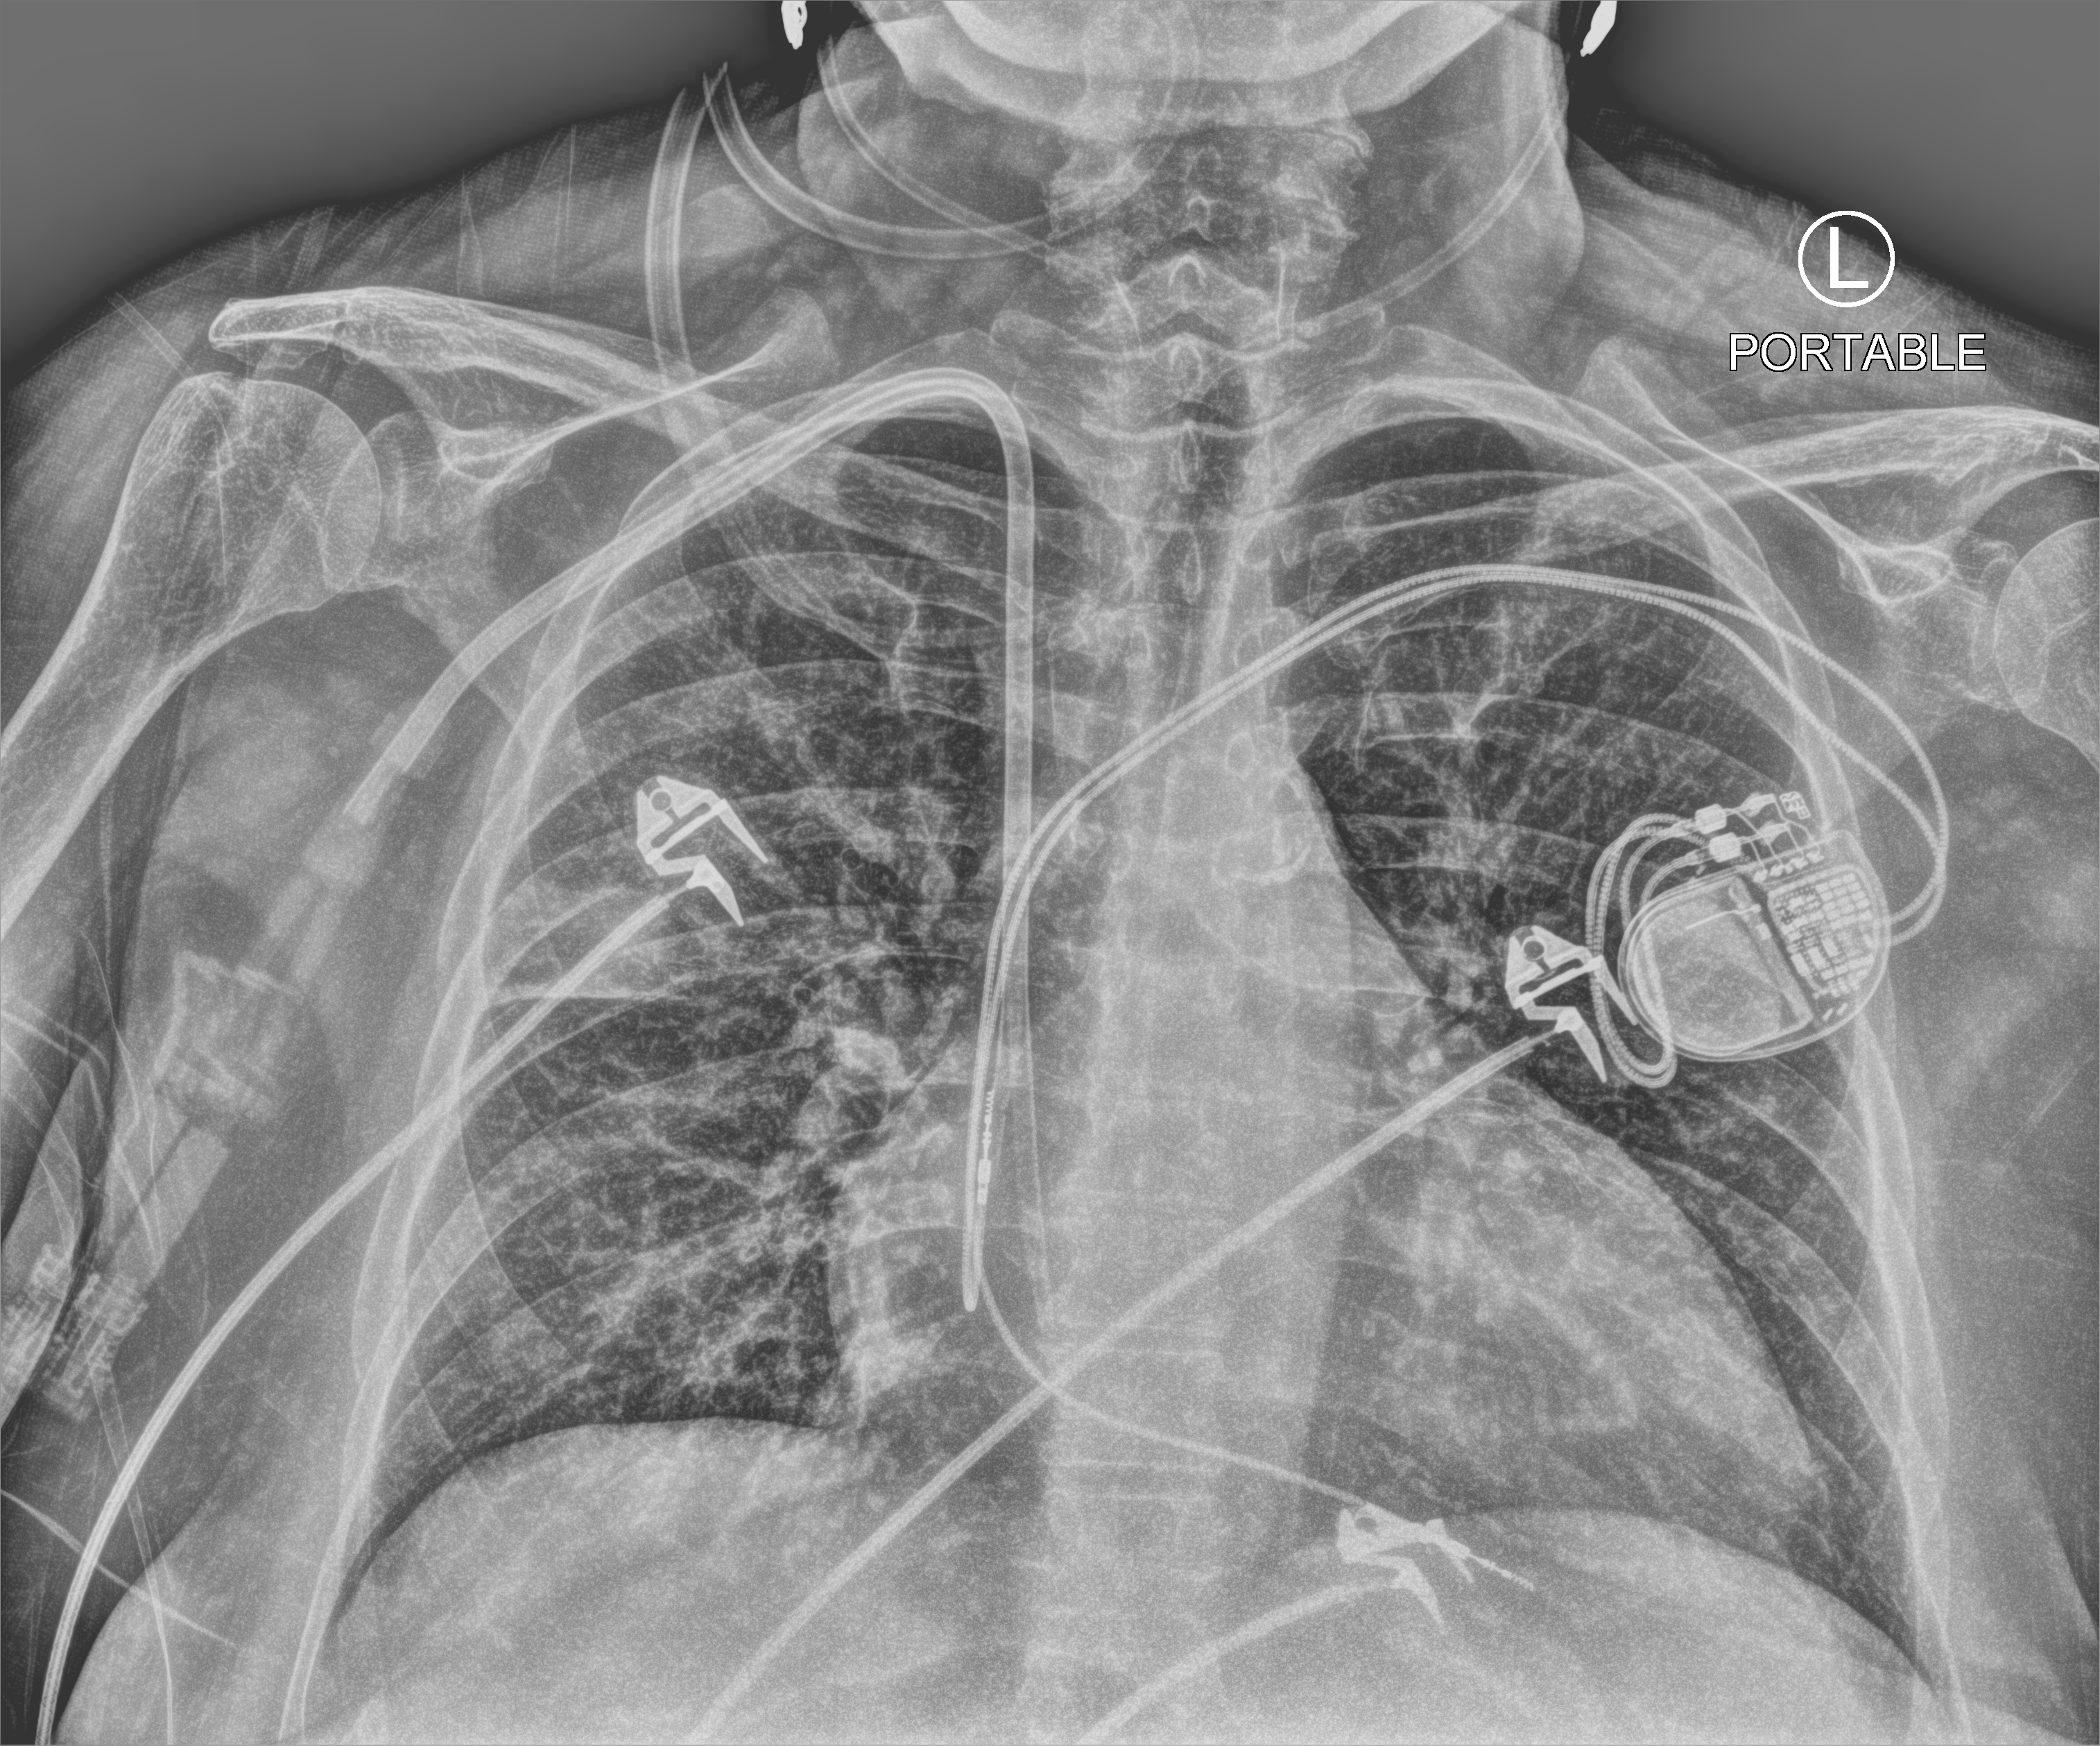
Chest X-ray (portable), anteroposterior (AP) projection. Female patient hospitalised with COVID-19, age 60–74 years.
Admission-level facts for this patient (not findings on this image; timing relative to this image not recorded):
- mechanically ventilated during this hospital stay: no
- length of hospital stay: 18 days
- admitted to intensive care during this hospital stay: no